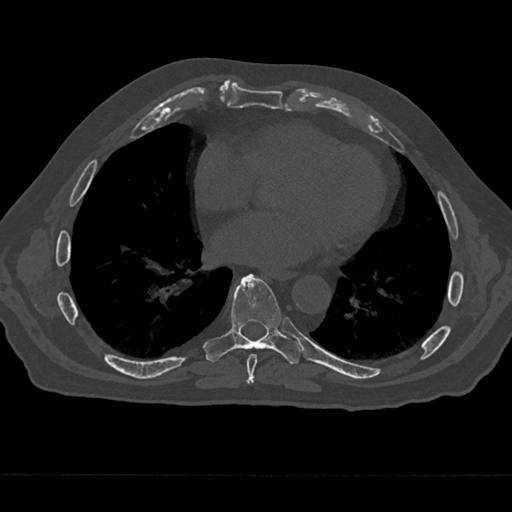
CT including the spine, one axial slice; position 330 of 797 along the scan axis; reconstruction kernel Br40s/3; 120 kVp; bone window (W 1800 / L 400 HU); 0.5 mm slice thickness; 512 × 512 image matrix. Male patient, age 75 years. Case-level facts recorded for this patient, not image findings: primary cancer: renal; vertebrae with lytic lesions (as recorded): T4.
Annotated regions visible in this slice (semi-automatically segmented with operator editing):
- T7 vertebra: bounding box <245,353,258,383> (left, top, right, bottom; pixels)
- T8 vertebra: <203,274,301,384>